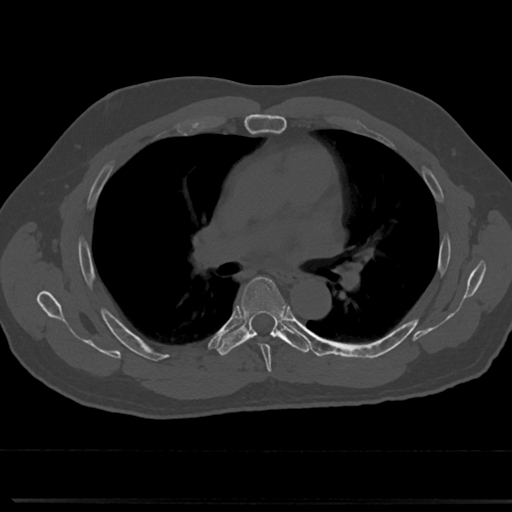
CT including the spine, one axial slice; position 469 of 817 along the scan axis; reconstruction kernel Br40s/3; 120 kVp; bone window (W 1800 / L 400 HU); 0.5 mm slice thickness; 512 × 512 image matrix. Male patient, age 61 years. From the clinical record (not read from this slice): primary cancer: prostate.
Structures marked on this image (semi-automatically segmented with operator editing):
- T5 vertebra: bounding box <241,277,285,362> (left, top, right, bottom; pixels)
- T6 vertebra: <219,275,286,354>